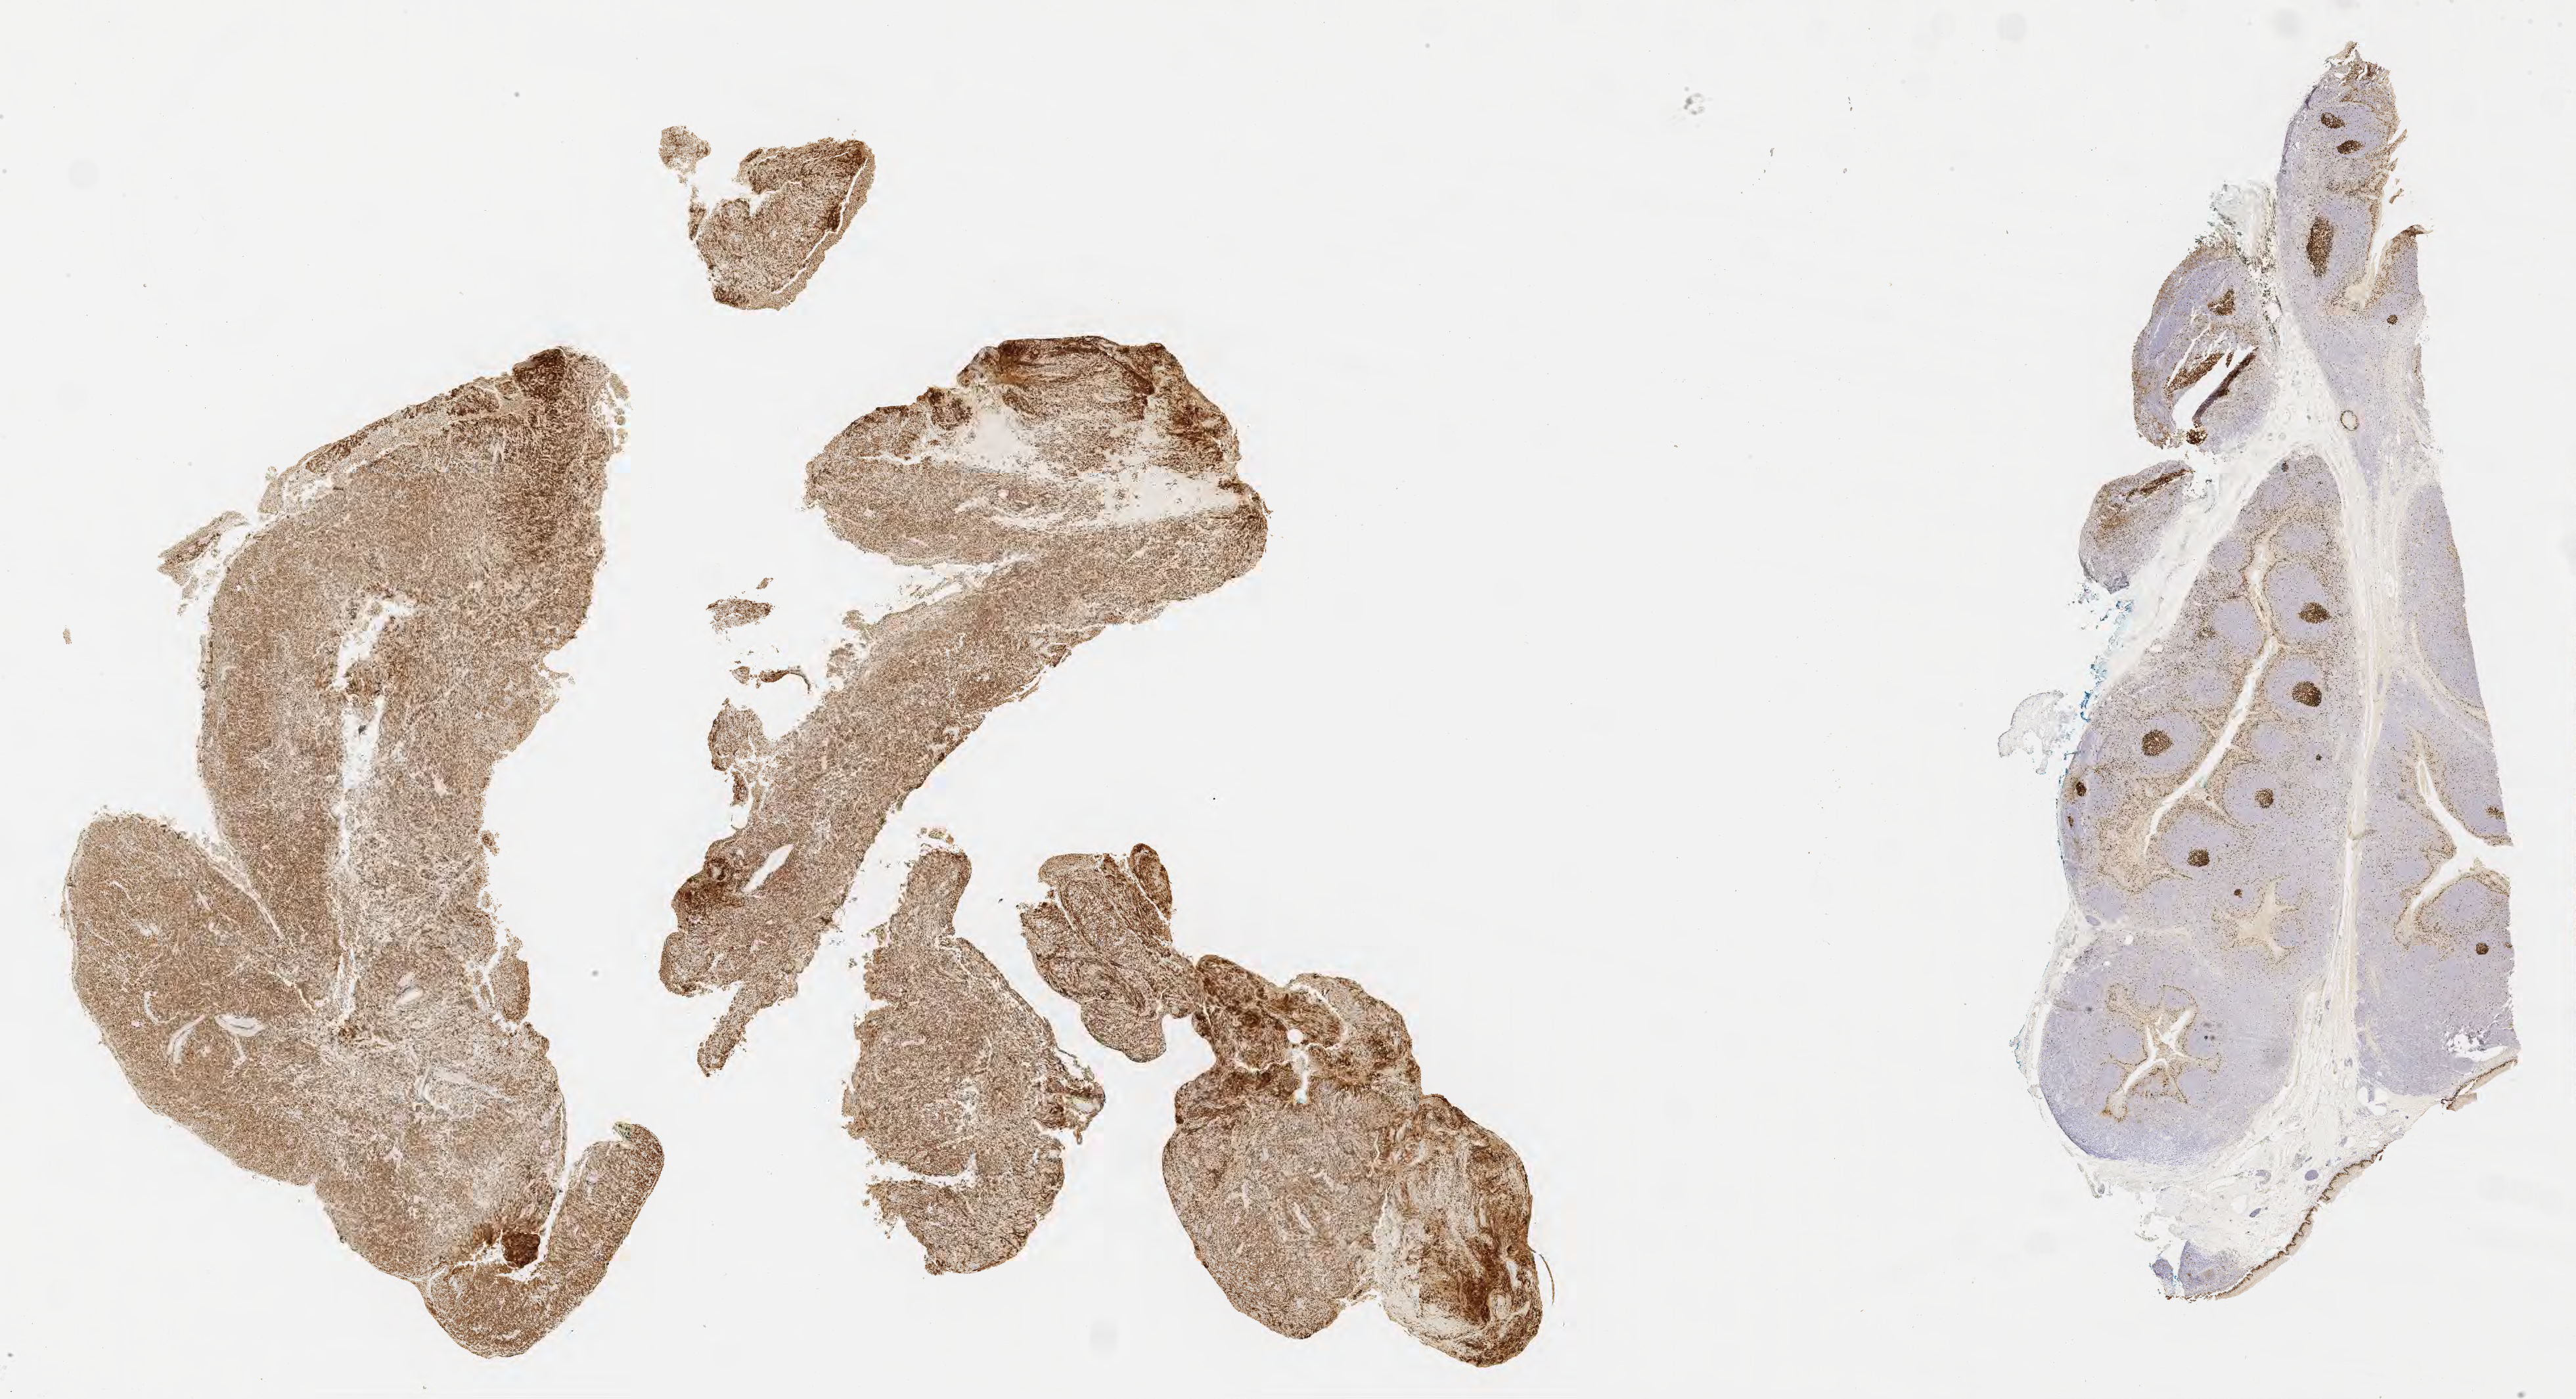
IHC for Ki-67, whole-slide image — low-resolution overview of the scanned area, about 31.7 x 17.2 mm, specimen: tumor tissue, anatomic site: abdomen proper. Male patient; age at initial diagnosis 5 years.
- diagnosis: Burkitt lymphoma, NOS